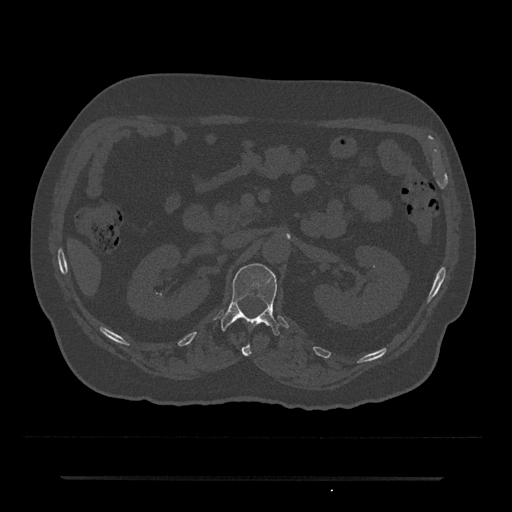
CT including the spine, one axial slice. Position 79 of 797 along the scan axis. Reconstruction kernel Br40s/3. 120 kVp. Bone window (W 1800 / L 400 HU). 0.5 mm slice thickness. 512 × 512 image matrix, field of view 437 × 437 mm. Patient: male, 69 years. Case-level facts recorded for this patient, not image findings: primary cancer: prostate.
Structures marked on this image (semi-automatically segmented with operator editing):
- L1 vertebra: box from (x=221, y=263) to (x=279, y=336) px
- T12 vertebra: (x=241, y=344)–(x=252, y=356)